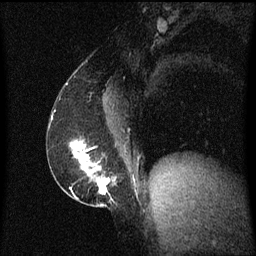
Breast MRI (dynamic contrast-enhanced), one sagittal slice; dynamic contrast-enhanced series, image 2 of 3 at this slice position (ordered by acquisition); 1.5 T; TE 4.2 ms, TR 8.4 ms; 2 mm slice thickness; 256 × 256 image matrix. Patient: female, 52 years. From the clinical record (not read from this slice): setting: breast cancer imaged before/during neoadjuvant chemotherapy; receptor status: HER2-positive.
Outlined on this slice (semi-automatic segmentation, software-assisted and operator-edited):
- analysis volume of interest (the breast-tissue region the enhancement analysis was run in; not a lesion): bounding box <62,138,117,203> (left, top, right, bottom; pixels)
- tumour enhancement mask (voxels above the 70 % enhancement threshold inside the analysis volume of interest): <71,142,111,195>